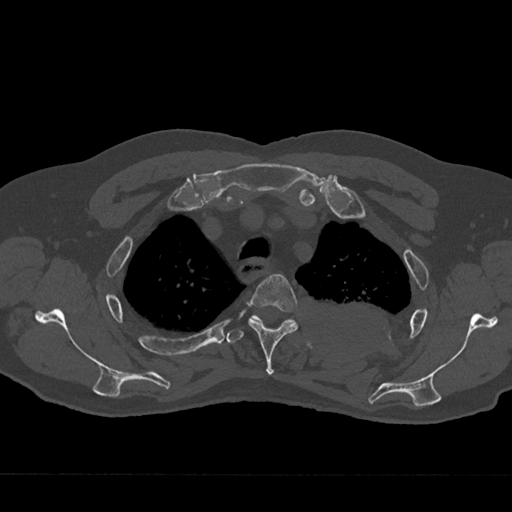
CT including the spine, one axial slice. Slice 557 of 797 in the series (ordered by position). Reconstruction kernel Br40s/3. Bone window (W 1800 / L 400 HU). 0.5 mm slice thickness. 512 × 512 image matrix. Patient: male, 75 years. From the clinical record (not read from this slice): primary cancer: renal; vertebrae with lytic lesions (as recorded): T4.
Outlined on this slice (semi-automatically segmented with operator editing):
- T3 vertebra: bounding box <248,274,298,375> (left, top, right, bottom; pixels)
- T4 vertebra: <227,315,296,343>